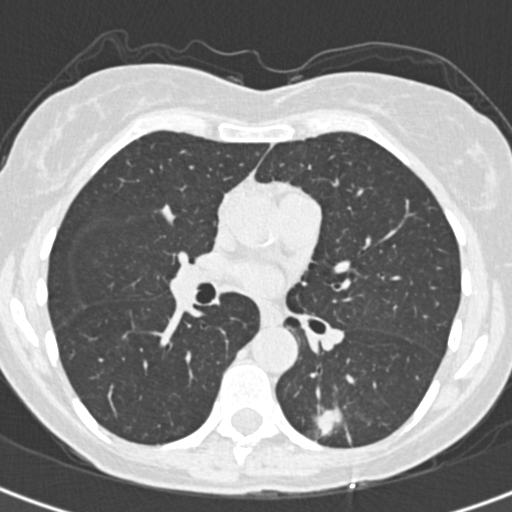
Low-dose screening chest CT, one axial slice; position 188 of 328 along the scan axis; 120 kVp; lung window (W 1500 / L -600 HU); 1 mm slice thickness; 512 × 512 image matrix, field of view 284 × 284 mm.
Structures marked on this image (manually delineated by an expert):
- lesion 1 (tumor, lower lobe of left lung): bounding box <315,409,342,436> (left, top, right, bottom; pixels)